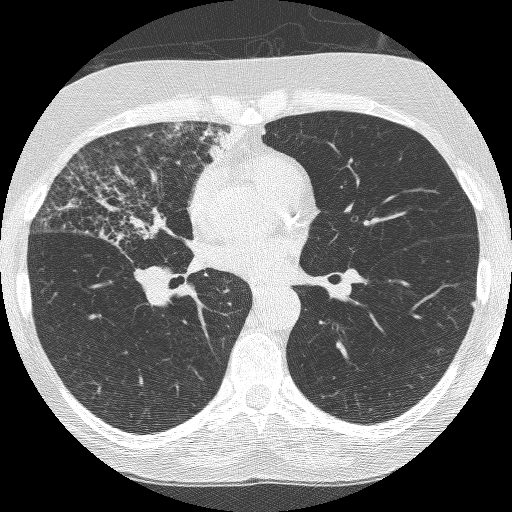
Axial slice from a low-dose chest CT screening exam; third screening round (two years after baseline); lung window (W 1500 / L -600 HU); lung (sharp) reconstruction kernel (BONE); 120 kVp; 512 × 512 image matrix, field of view 294 × 294 mm. Female, age 64 years at enrolment. Former smoker at enrolment.
Lesion marked by an expert reader, bounding box <55,161,199,308> (left, top, right, bottom; pixels). Reader record for this screening exam (exam-level; its link to the box is not recorded): non-calcified nodule or mass ≥4 mm, right upper lobe, 49 × 43 mm, spiculated (stellate) margins, soft tissue attenuation, pre-existing on the prior screen: yes; interval growth: yes. Lung cancer was diagnosed 7 days after this screen: adenocarcinoma, NOS, right upper lobe, right middle lobe, right hilum, stage IV (AJCC 6th edition), 85 mm at pathology.